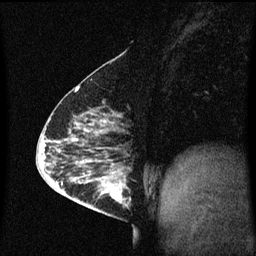
Breast MRI (dynamic contrast-enhanced), one sagittal slice. Position 26 of 60 along the scan axis. Dynamic contrast-enhanced series, image 2 of 3 at this slice position (ordered by acquisition). 1.5 T. TE 4.2 ms, TR 8.4 ms. 256 × 256 image matrix, field of view 200 × 200 mm. Patient: female, 63 years.
Annotated regions visible in this slice (semi-automatically segmented with operator editing):
- analysis volume of interest (the breast-tissue region the enhancement analysis was run in; not a lesion): bounding box (x1, y1, x2, y2) in pixels: (98, 168, 133, 217)
- tumour enhancement mask (voxels above the 70 % enhancement threshold inside the analysis volume of interest): (98, 168, 127, 205)